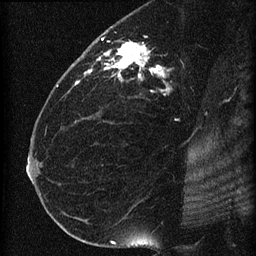
Breast MRI (dynamic contrast-enhanced), one sagittal slice. Slice 36 of 60 in the series (ordered by position). Dynamic contrast-enhanced series, image 2 of 4 at this slice position (ordered by acquisition). 1.5 T. TE 4.2 ms, TR 22.7 ms. 1.5 mm slice thickness. 256 × 256 image matrix, field of view 180 × 180 mm. Female patient, age 35 years. Case-level facts recorded for this patient, not image findings: setting: breast cancer imaged before/during neoadjuvant chemotherapy; receptor status: HR-positive, HER2-negative.
Outlined on this slice (semi-automatic segmentation, software-assisted and operator-edited):
- analysis volume of interest (the breast-tissue region the enhancement analysis was run in; not a lesion): bounding box <69,27,199,112> (left, top, right, bottom; pixels)
- tumour enhancement mask (voxels above the 90 % enhancement threshold inside the analysis volume of interest): <75,38,170,92>